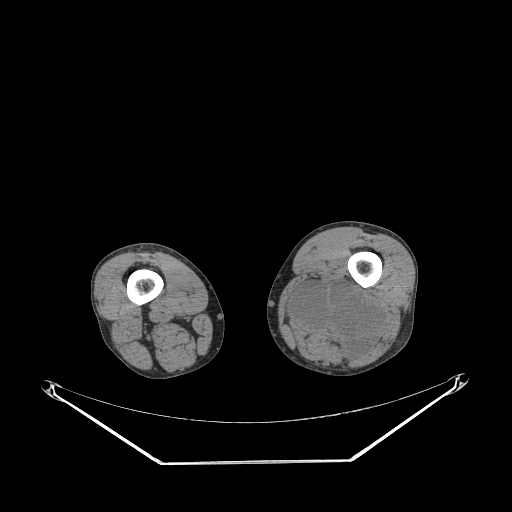
CT of an extremity soft-tissue mass (from a PET/CT study), one axial slice; position 212 of 267 along the scan axis; 140 kVp; soft-tissue window (W 400 / L 40 HU); 3.75 mm slice thickness; 512 × 512 image matrix, field of view 500 × 500 mm. Male patient. From the clinical record (not read from this slice): histological type: undifferentiated pleomorphic liposarcoma; grade: high; site of the primary tumour: left thigh.
Outlined on this slice (expert contour drawn on MRI and transferred to this co-registered scan by the dataset authors):
- gross tumour volume including surrounding oedema: bounding box (x1, y1, x2, y2) in pixels: (288, 272, 380, 357)
- gross tumour volume (mass): (295, 285, 375, 348)